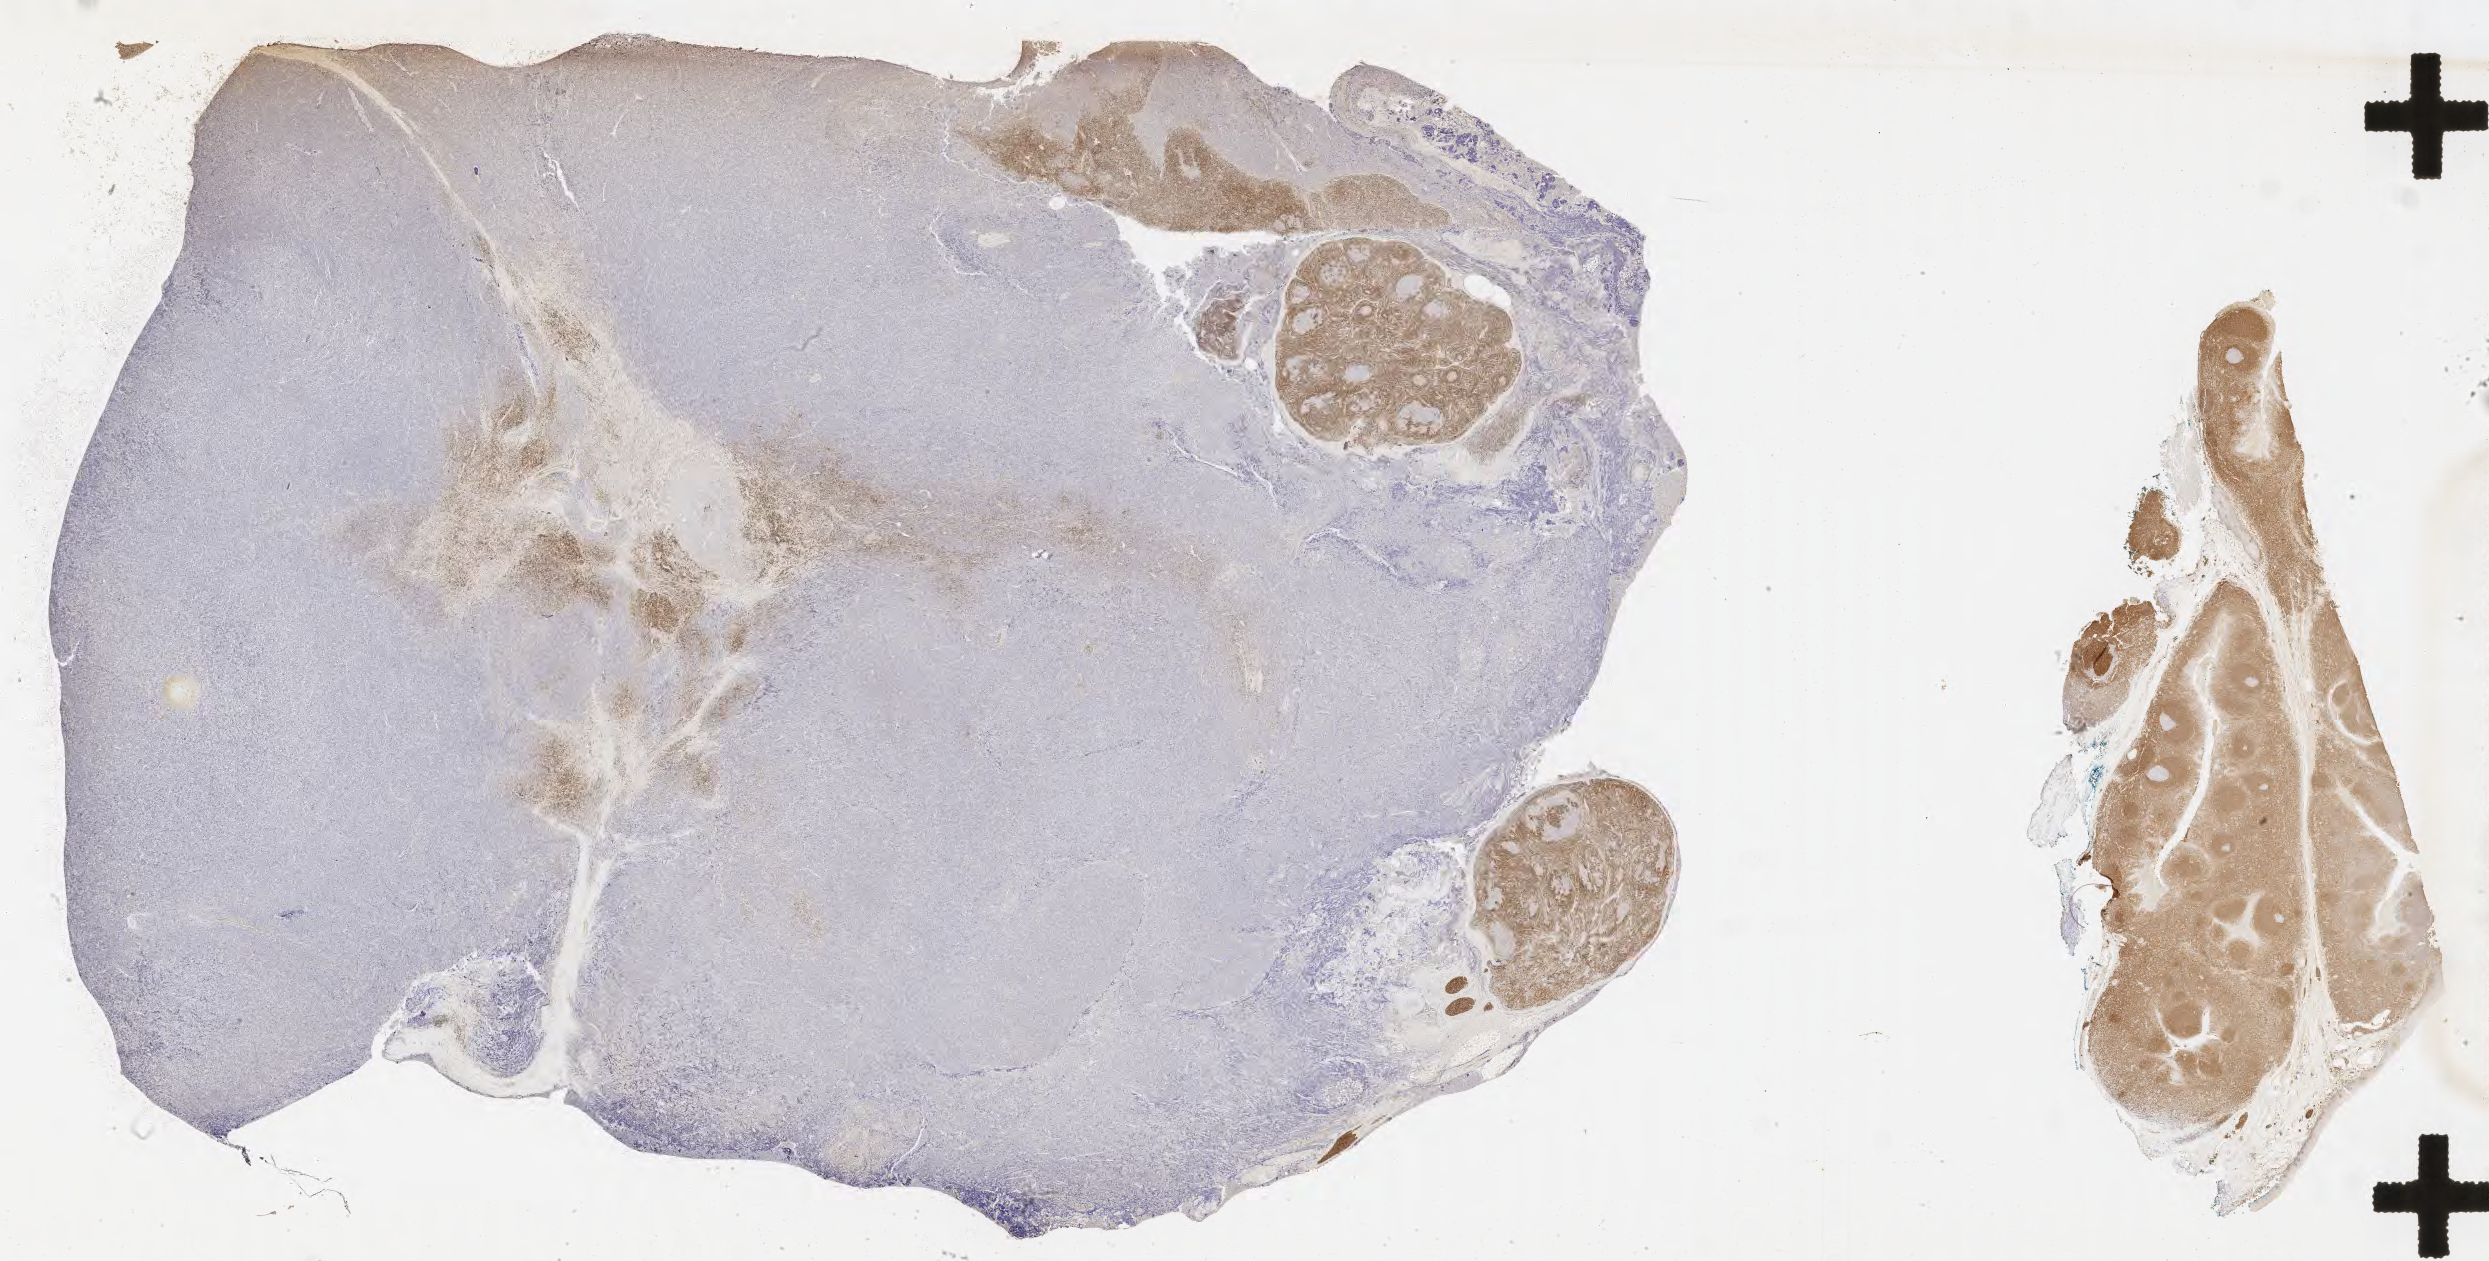
IHC for BCL2, whole-slide image, shown as a low-resolution overview of the whole scanned area (about 40.3 x 20.4 mm), specimen: tumor tissue, site: lymph node of head and neck. Male patient; age at initial diagnosis 3 years.
Histologic diagnosis: Burkitt lymphoma, NOS.